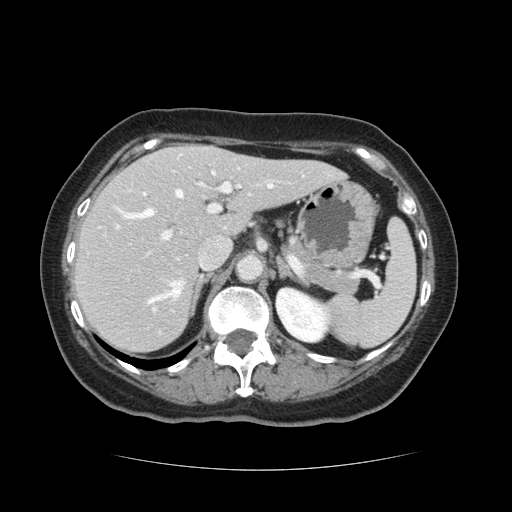
Contrast-enhanced abdominal CT, one axial slice. 120 kVp. Intravenous contrast given. Soft-tissue window (W 400 / L 40 HU). 2.5 mm slice thickness. 512 × 512 image matrix. Female patient, age 67 years. Case-level facts recorded for this patient, not image findings: diagnosis: colorectal cancer liver metastases, imaged before liver resection; multiple liver metastases: yes; largest metastasis: 3 cm; chemotherapy before resection: no.
Structures marked on this image (expert manual segmentation):
- hepatic veins: bounding box (x1, y1, x2, y2) in pixels: (119, 185, 273, 303)
- liver: (74, 146, 340, 353)
- planned liver remnant (the part of the liver to remain after resection): (74, 157, 341, 353)
- portal vein (with intrahepatic branches): (116, 170, 272, 241)